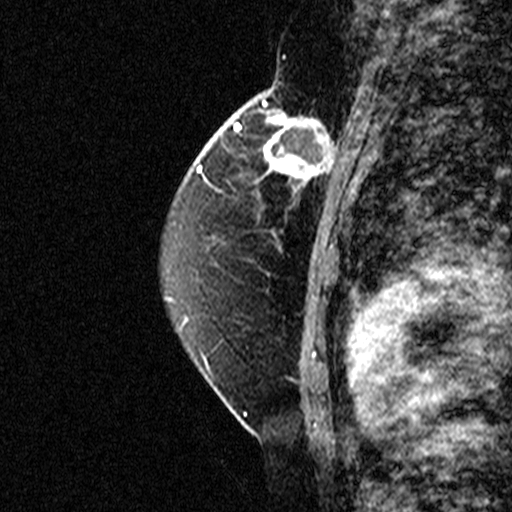
Breast MRI (dynamic contrast-enhanced), one sagittal slice; slice 27 of 44 in the series (ordered by position); dynamic contrast-enhanced study with each time point stored as its own series, time point 2 of 3 at this slice position (early post-contrast, ordered by acquisition time); 1.5 T; TE 4.5 ms, TR 11 ms; 3 mm slice thickness; 512 × 512 image matrix, field of view 200 × 200 mm. Patient: female, 49 years. Case-level facts recorded for this patient, not image findings: setting: breast cancer imaged before/during neoadjuvant chemotherapy; receptor status: triple-negative.
Outlined on this slice (semi-automatic segmentation, software-assisted and operator-edited):
- analysis volume of interest (the breast-tissue region the enhancement analysis was run in; not a lesion): bounding box <254,112,347,207> (left, top, right, bottom; pixels)
- tumour enhancement mask (voxels above the 90 % enhancement threshold inside the analysis volume of interest): <254,112,347,207>